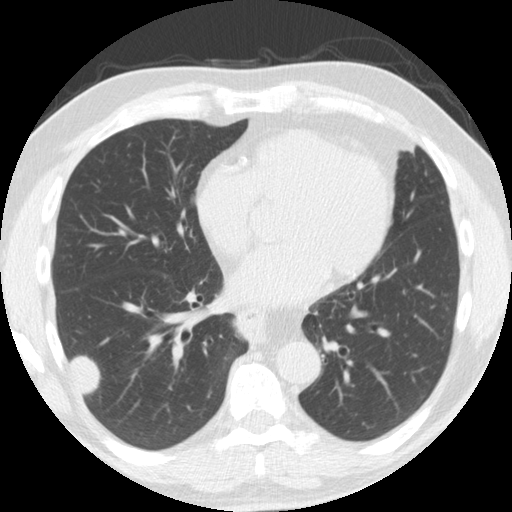
Axial slice from a low-dose chest CT screening exam; second screening round (one year after baseline); lung window (W 1500 / L -600 HU); 2.5 mm slice thickness; standard (soft-tissue) reconstruction kernel (STANDARD); 120 kVp; 512 × 512 image matrix. Male participant, aged 61 years at enrolment. Former smoker at enrolment.
Lesion marked by an expert reader, bounding box <45,322,113,399> (left, top, right, bottom; pixels). Reader record for this screening exam (exam-level; its link to the box is not recorded): non-calcified nodule or mass ≥4 mm, right lower lobe, 33 × 19 mm, smooth margins, soft tissue attenuation, pre-existing on the prior screen: yes; interval growth: yes. Participant outcome: lung cancer diagnosed 30 days after this screen — adenosquamous carcinoma, right lower lobe, poorly differentiated (G3), stage IV (AJCC 6th edition), 45 mm at pathology.